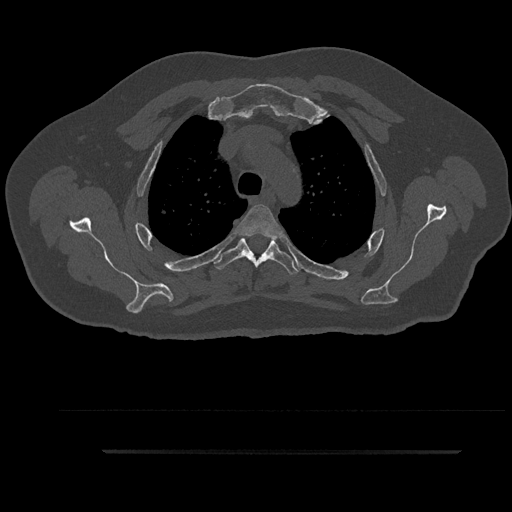
CT including the spine, one axial slice; slice 693 of 797 in the series (ordered by position); reconstruction kernel Br40s/3; bone window (W 1800 / L 400 HU); 0.5 mm slice thickness; 512 × 512 image matrix, field of view 432 × 432 mm. Patient: male, 63 years. From the clinical record (not read from this slice): primary cancer: renal; vertebrae with lytic lesions (as recorded): T8.
Structures marked on this image (semi-automatically segmented with operator editing):
- T3 vertebra: bounding box <236,204,282,238> (left, top, right, bottom; pixels)
- T4 vertebra: <213,236,300,274>